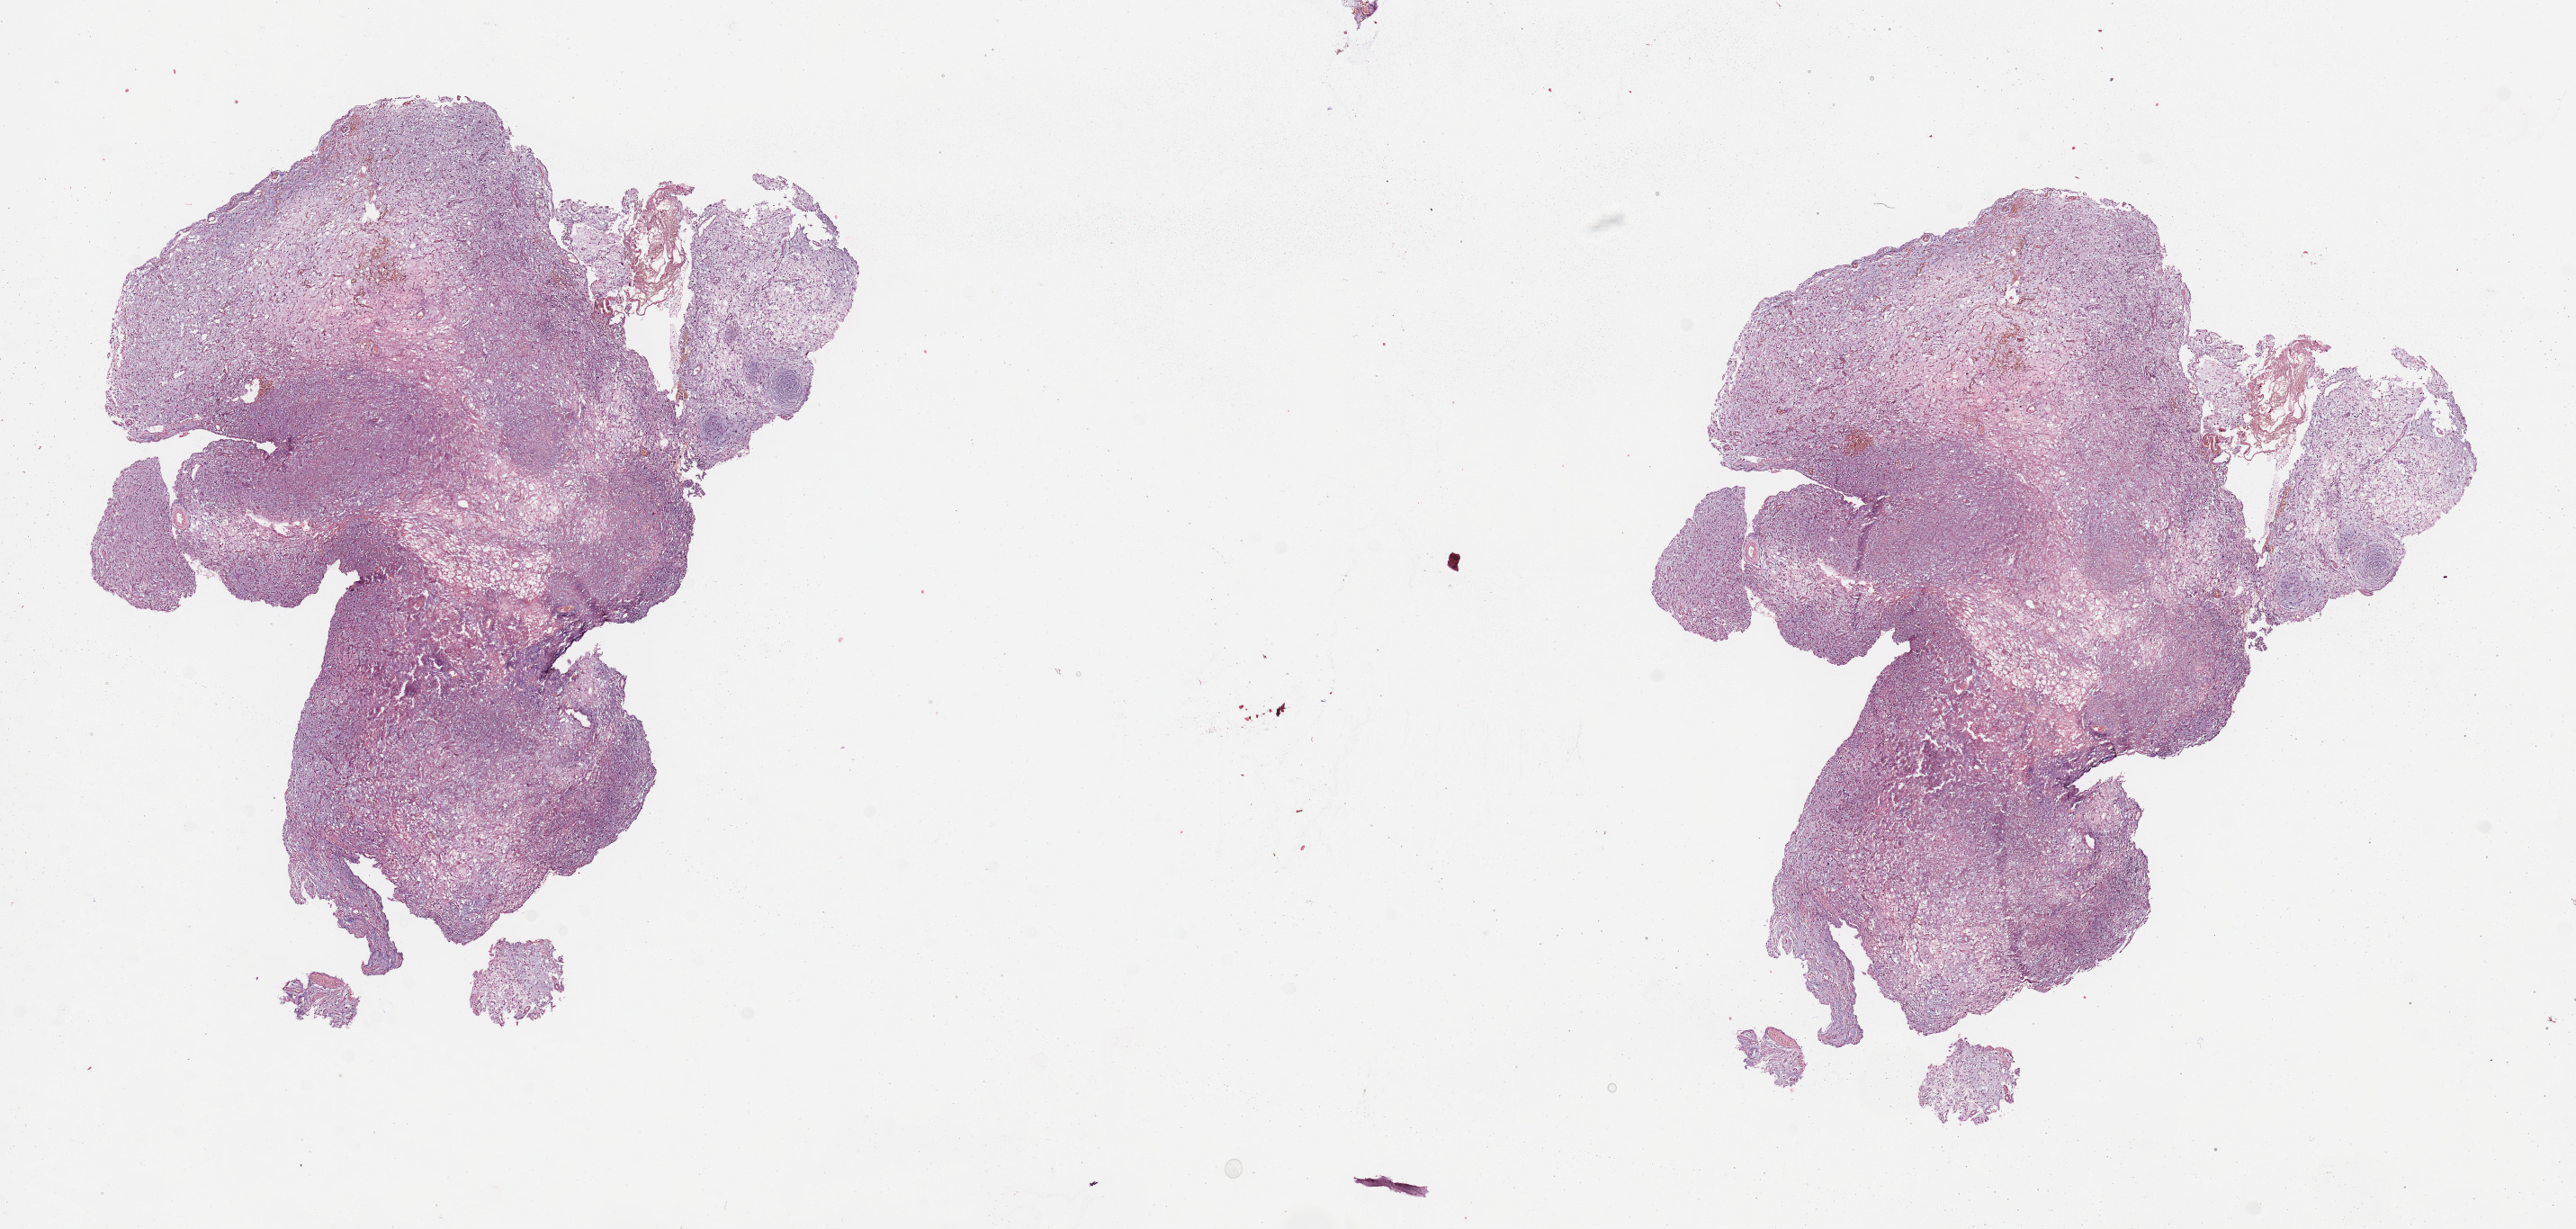
Whole-slide histology image, H&E, low-resolution overview of the scanned area, about 22.6 x 10.8 mm. Male, 20 y/o.
Patient diagnosis (cohort enrolment): sarcoma (site not recorded at cohort level).